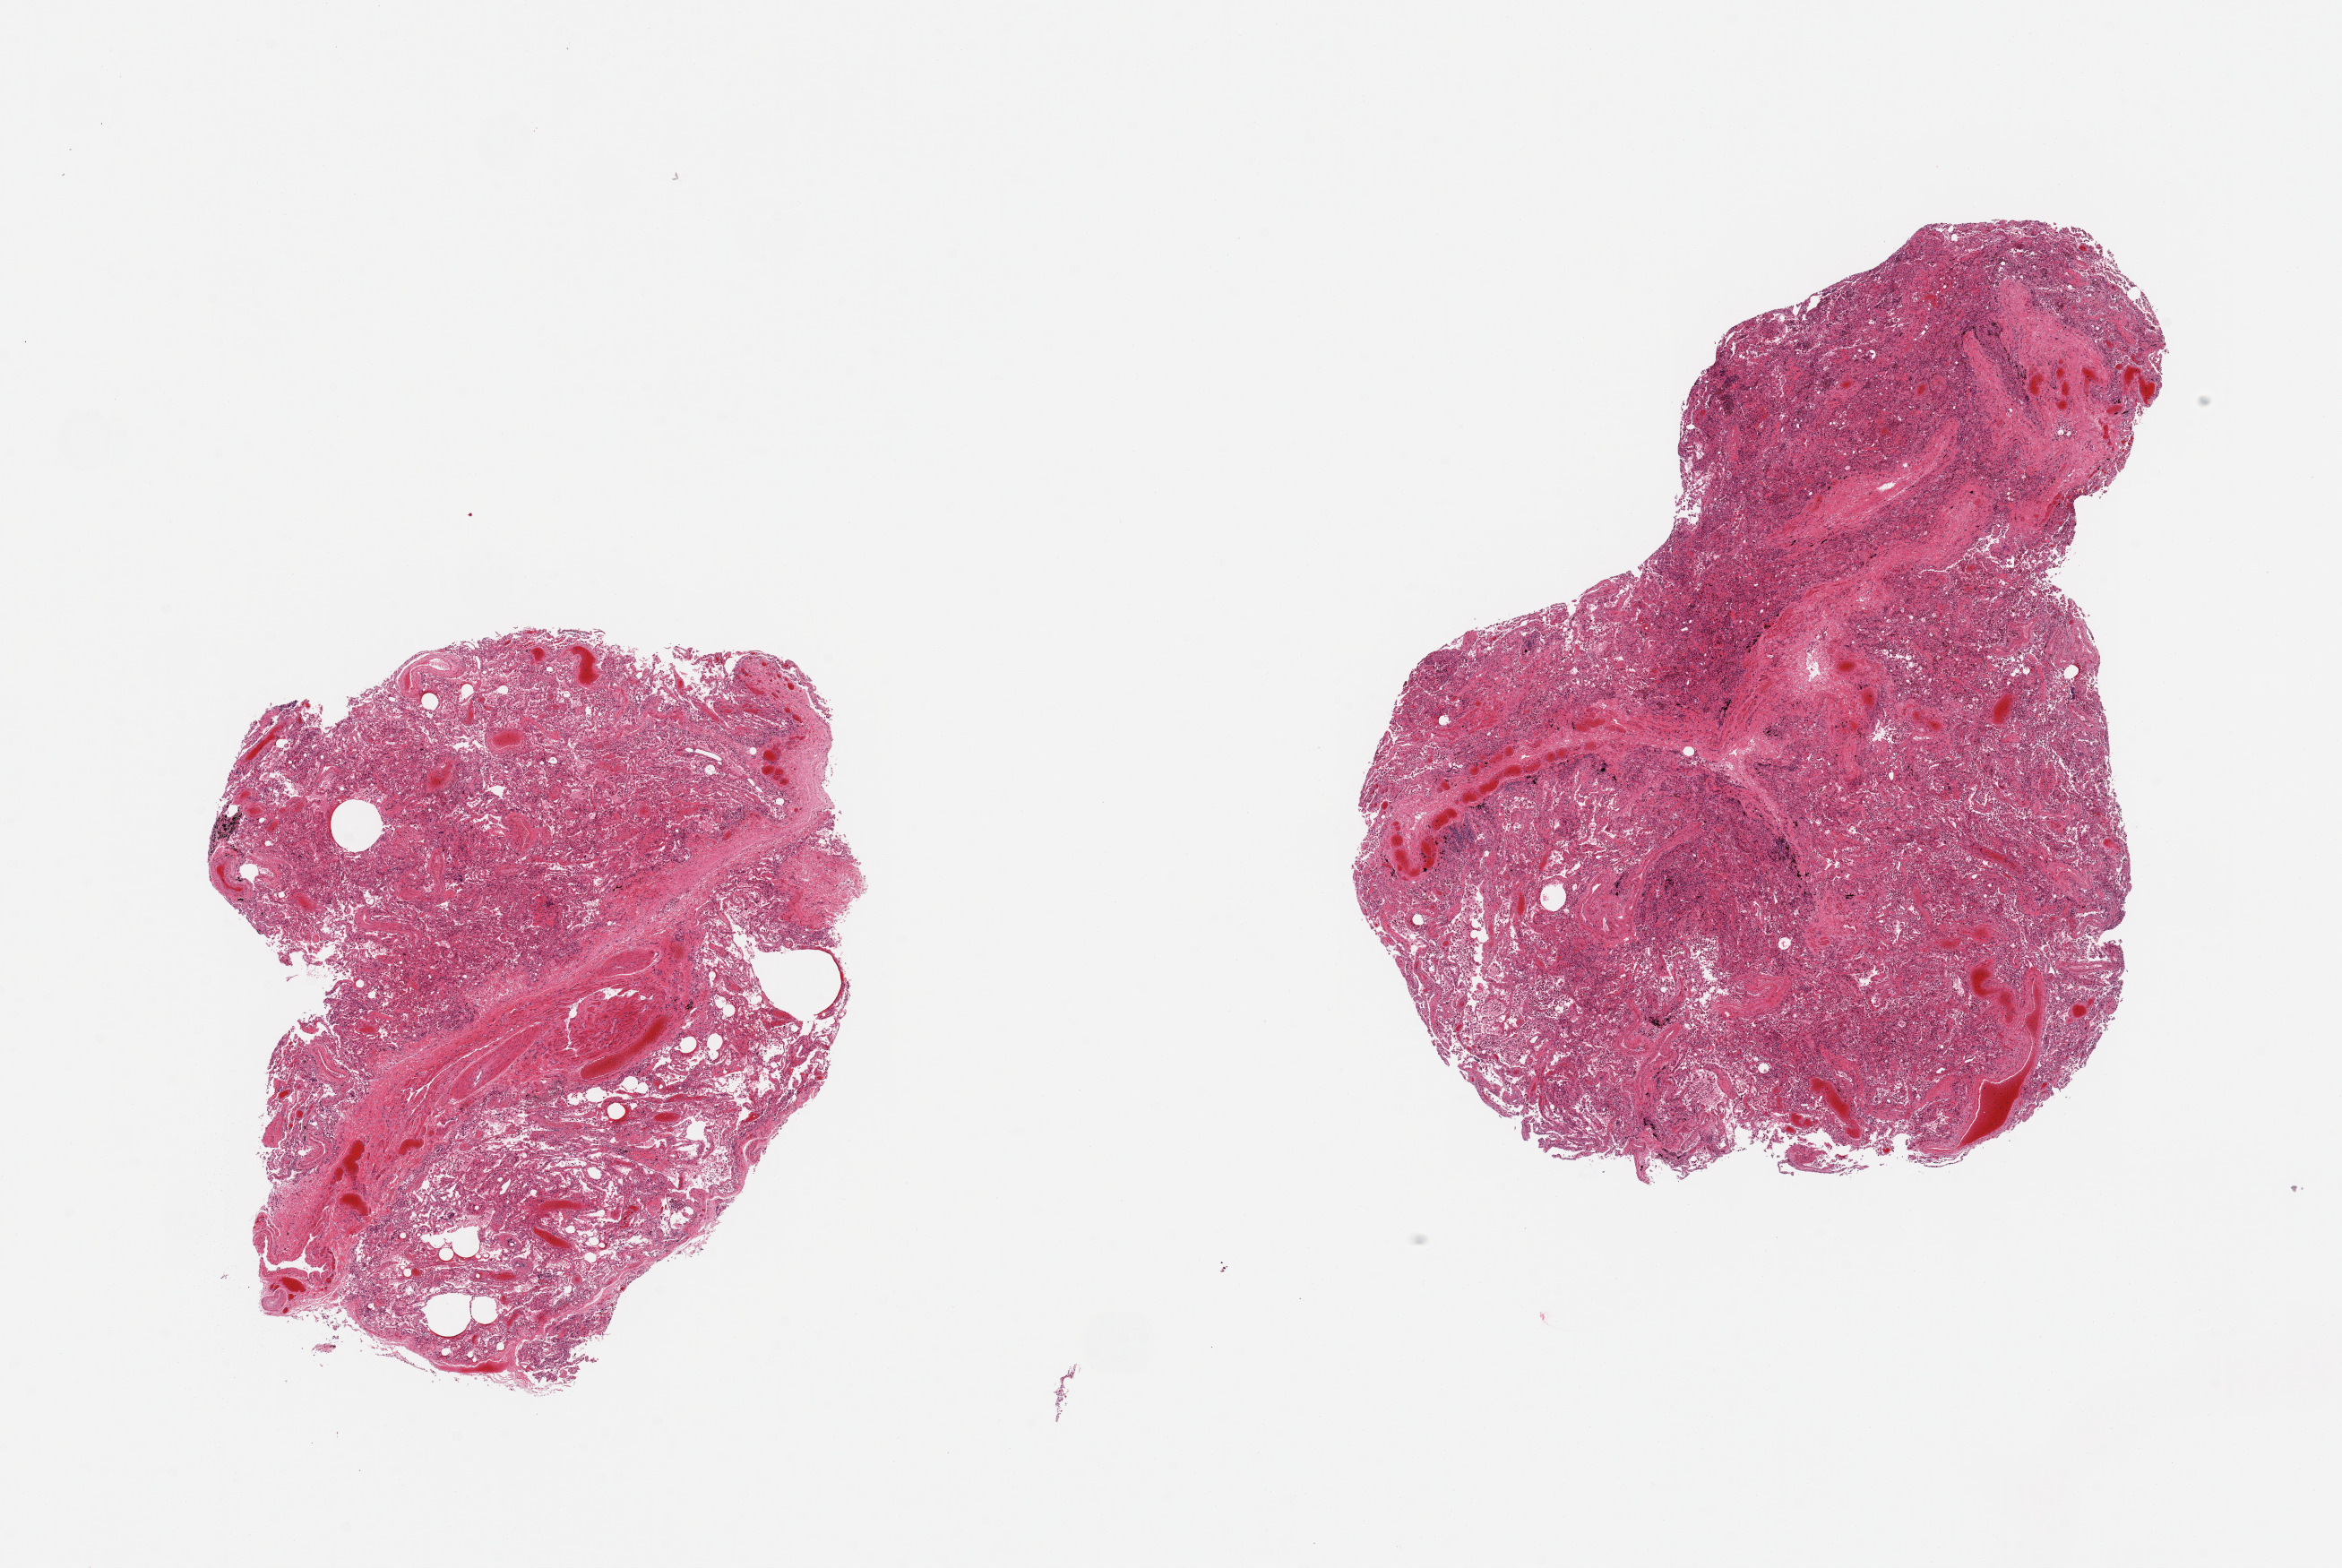
H&E whole-slide image, shown as a low-resolution overview of the whole scanned area (about 20.7 x 13.8 mm, from a 20x scan). PAXgene-fixed paraffin-embedded (PFPE) section. Target tissue: lung. Donor tissue sample.
- review note (as recorded): 2 pieces; congestion, collapse, numerous macrophages, some fibrosis